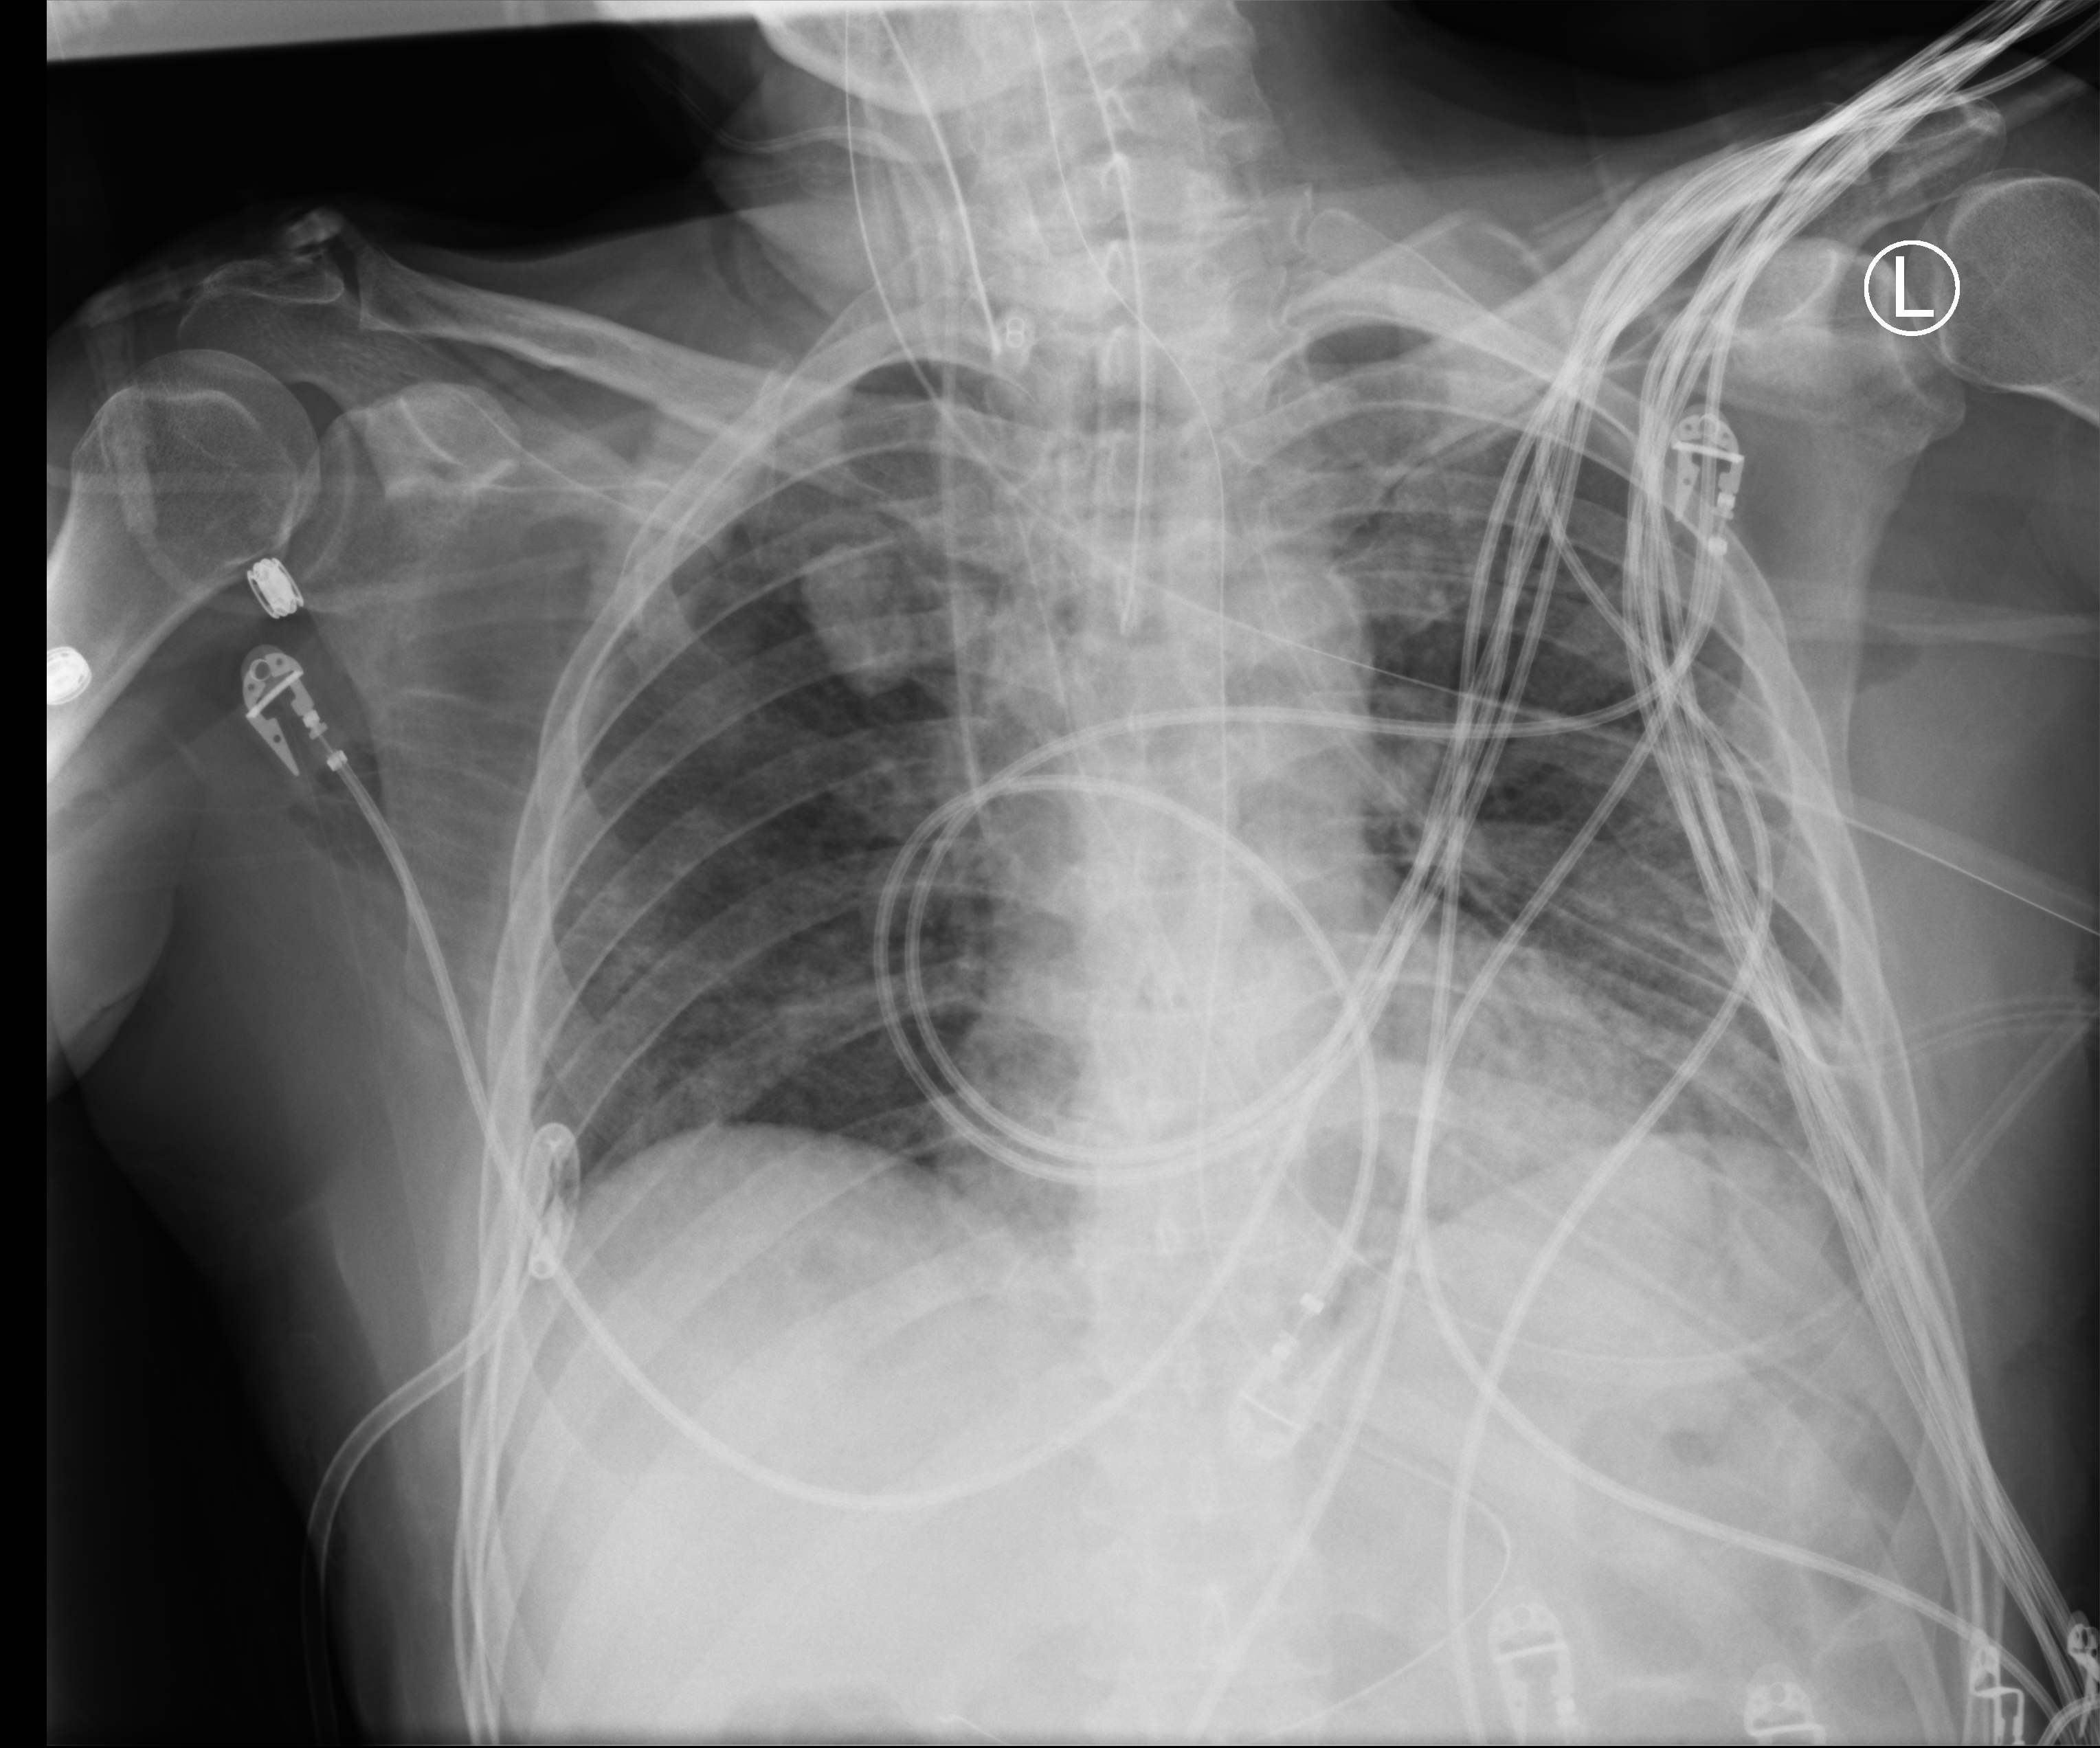
Chest X-ray (portable); anteroposterior (AP) projection. Patient hospitalised with COVID-19; male, aged 18–59 years.
From the hospital-stay record, not from the radiograph (when in the stay this image was taken is not recorded): chronic kidney disease (admission record): no.